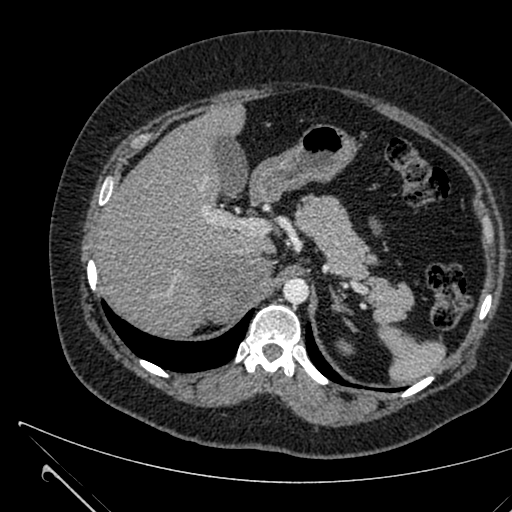
Contrast-enhanced abdominal CT, one axial slice. Slice 462 of 731 in the series (ordered by position). 120 kVp. Intravenous contrast given. Soft-tissue window (W 400 / L 40 HU). 1 mm slice thickness. 512 × 512 image matrix. Patient: female, 36 years. Case-level facts recorded for this patient, not image findings: diagnosis: adrenocortical carcinoma; tumour side: right adrenal; tumour size at pathology: 10 cm; Ki-67 index: 20 %; stage (as recorded): 4.
Outlined on this slice (semi-automatic segmentation, software-assisted and operator-edited):
- mass: bounding box <205,256,269,320> (left, top, right, bottom; pixels)